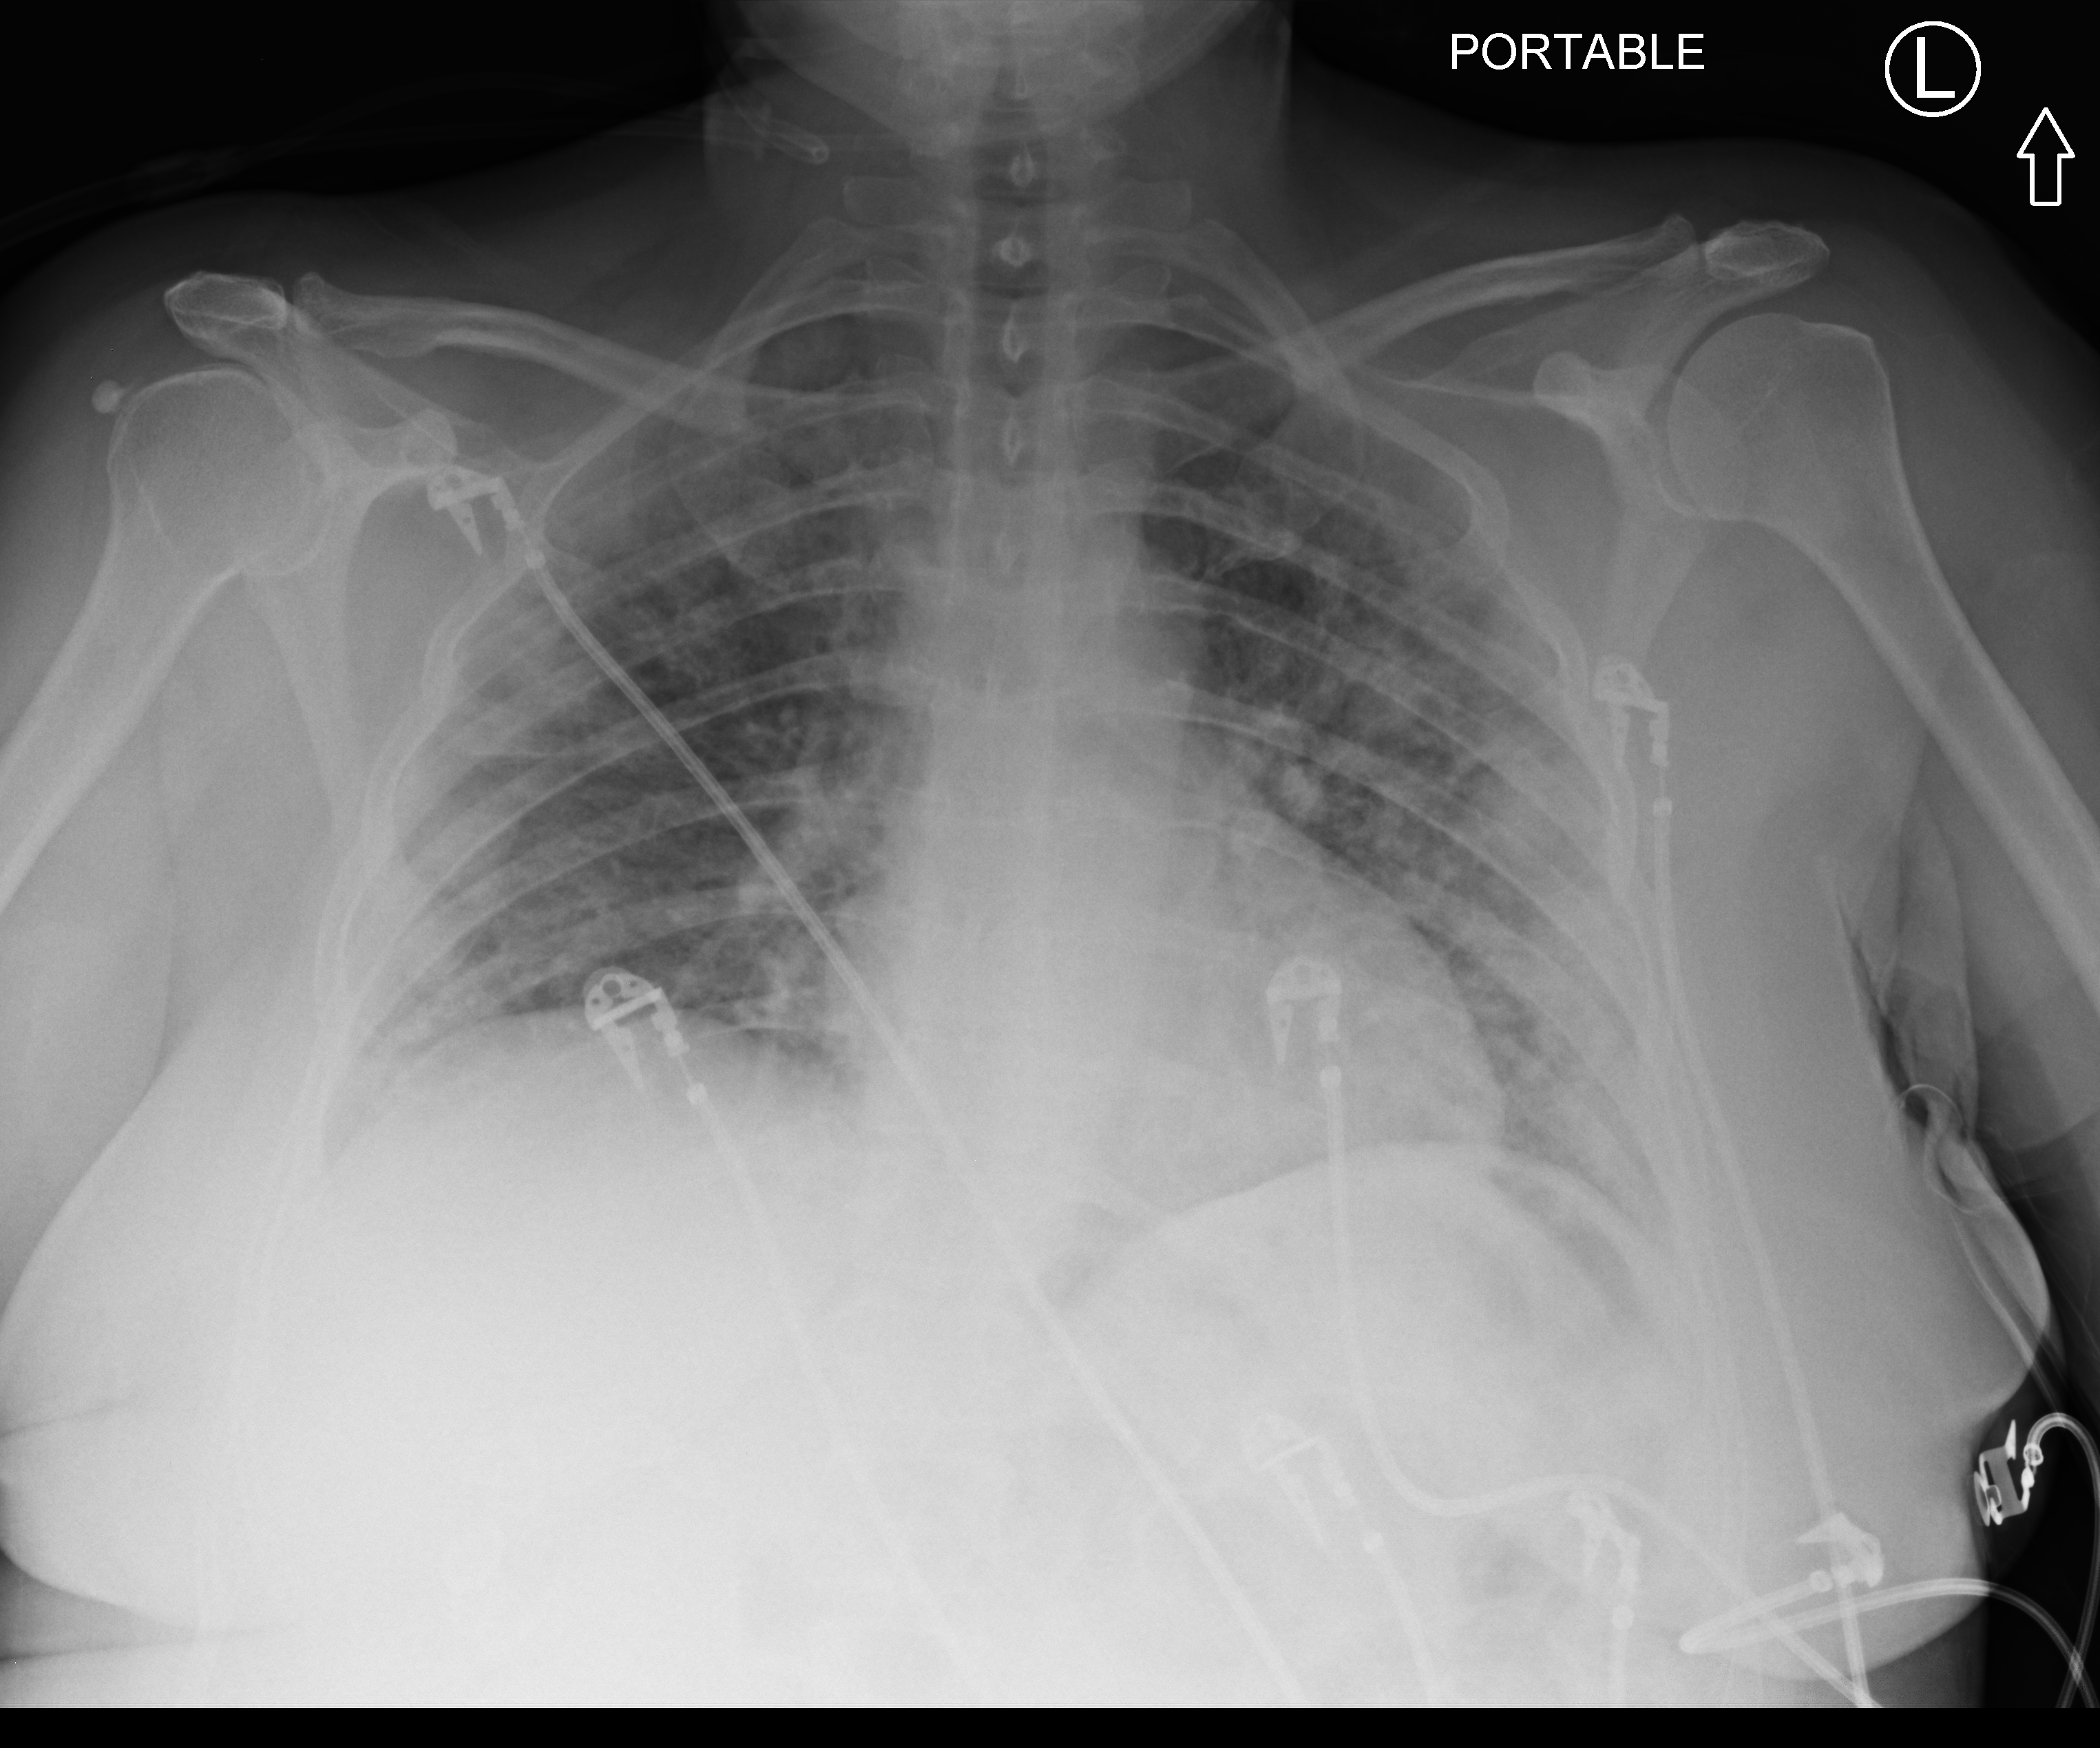
Chest X-ray (portable), anteroposterior (AP) projection. Female patient hospitalised with COVID-19, age 18–59 years.
Admission-level facts for this patient (not findings on this image; timing relative to this image not recorded): other chronic lung disease (admission record): no; mechanically ventilated during this hospital stay: no.